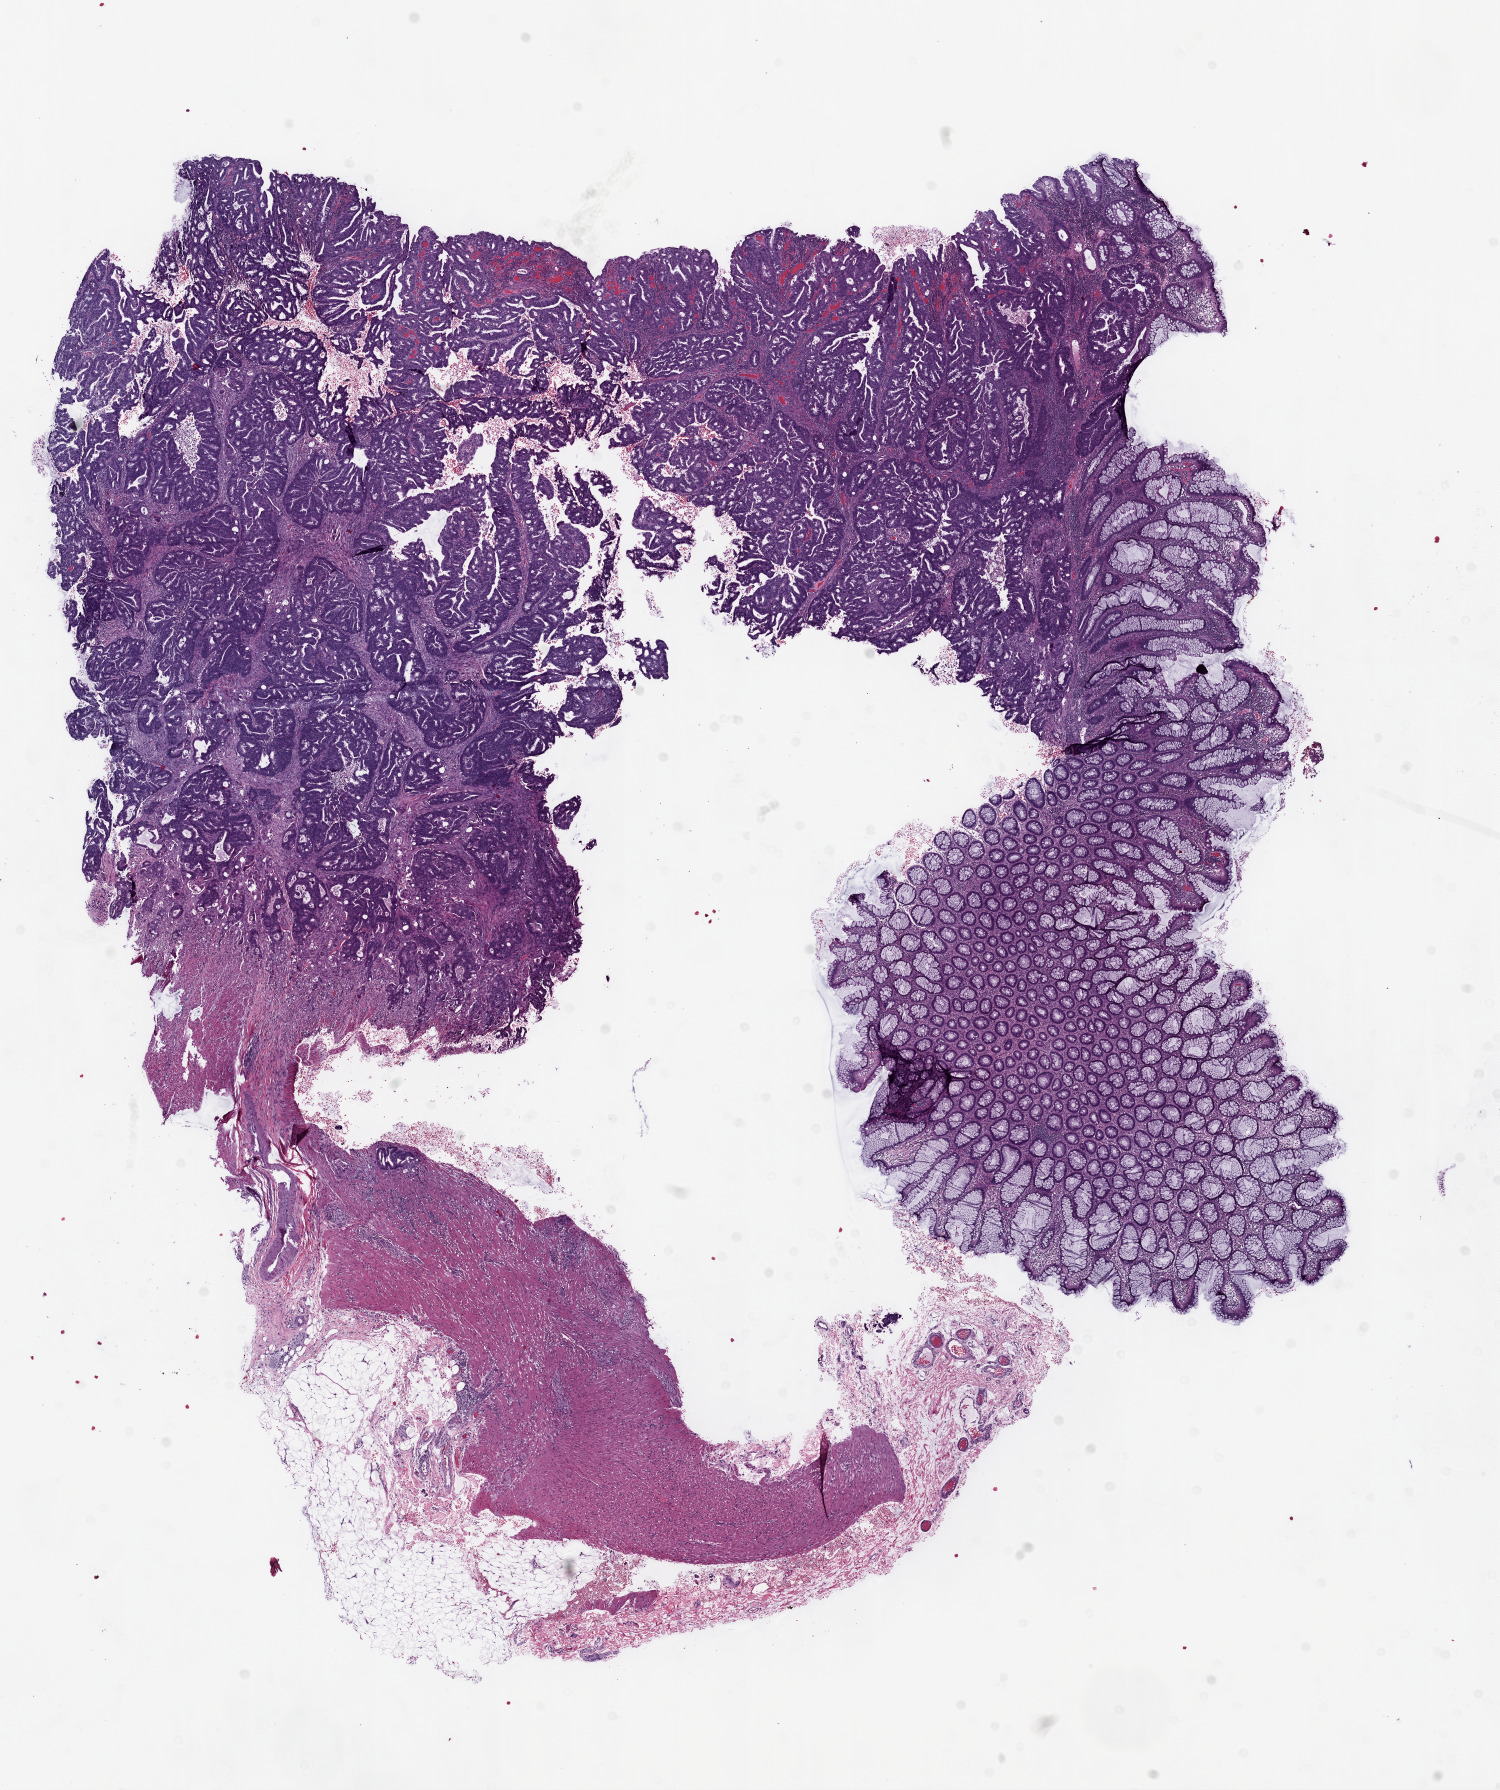
H&E whole-slide image, a low-resolution overview of the entire scanned area, about 12.0 x 14.4 mm (acquisition: 20x scan), frozen section, sample: primary tumour, colon. Patient: female, age at initial diagnosis 48 years. Composition of this section per pathologist review: tumour cells 64%, tumour nuclei 75%, normal cells 30%, stromal cells 5%, necrosis 1%.
AJCC pathologic stage: IIA (6th edition). Histologic diagnosis: Adenocarcinoma, NOS. Lymph nodes positive (case pathology): 0 of 29 examined.